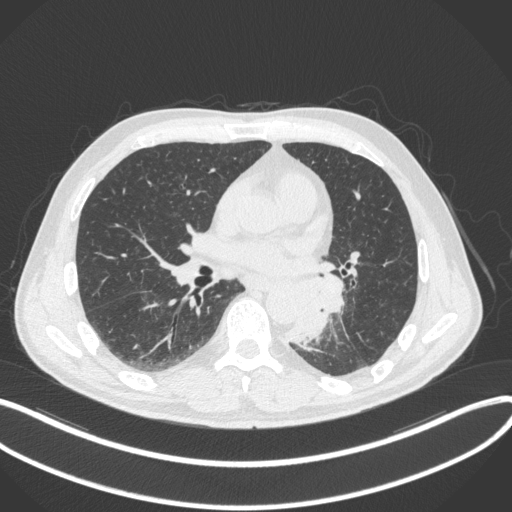
Chest CT, one axial slice; slice 164 of 328 in the series (ordered by position); reconstruction kernel B31f; lung window (W 1500 / L -600 HU); 1 mm slice thickness; 512 × 512 image matrix, field of view 400 × 400 mm. Patient: male, 59 years. Case-level facts recorded for this patient, not image findings: clinical TNM (as recorded): T2a N2 M0.
Outlined on this slice (bounding box drawn by a radiologist):
- lung tumour (recorded histology: squamous cell carcinoma): box from (x=283, y=273) to (x=343, y=345) px